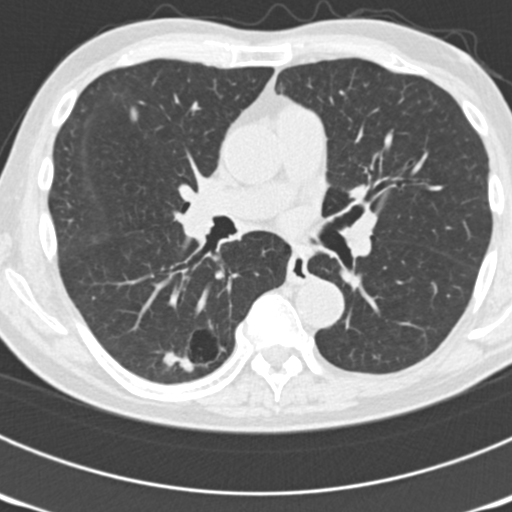
Low-dose screening chest CT, one axial slice; position 103 of 177 along the scan axis; reconstruction kernel B30f; 120 kVp; lung window (W 1500 / L -600 HU); 2 mm slice thickness; 512 × 512 image matrix, field of view 300 × 300 mm.
Annotated regions visible in this slice (manually delineated by an expert):
- lesion 5 (nodule, lower lobe of right lung): bounding box [x1, y1, x2, y2] px = [162, 349, 194, 375]